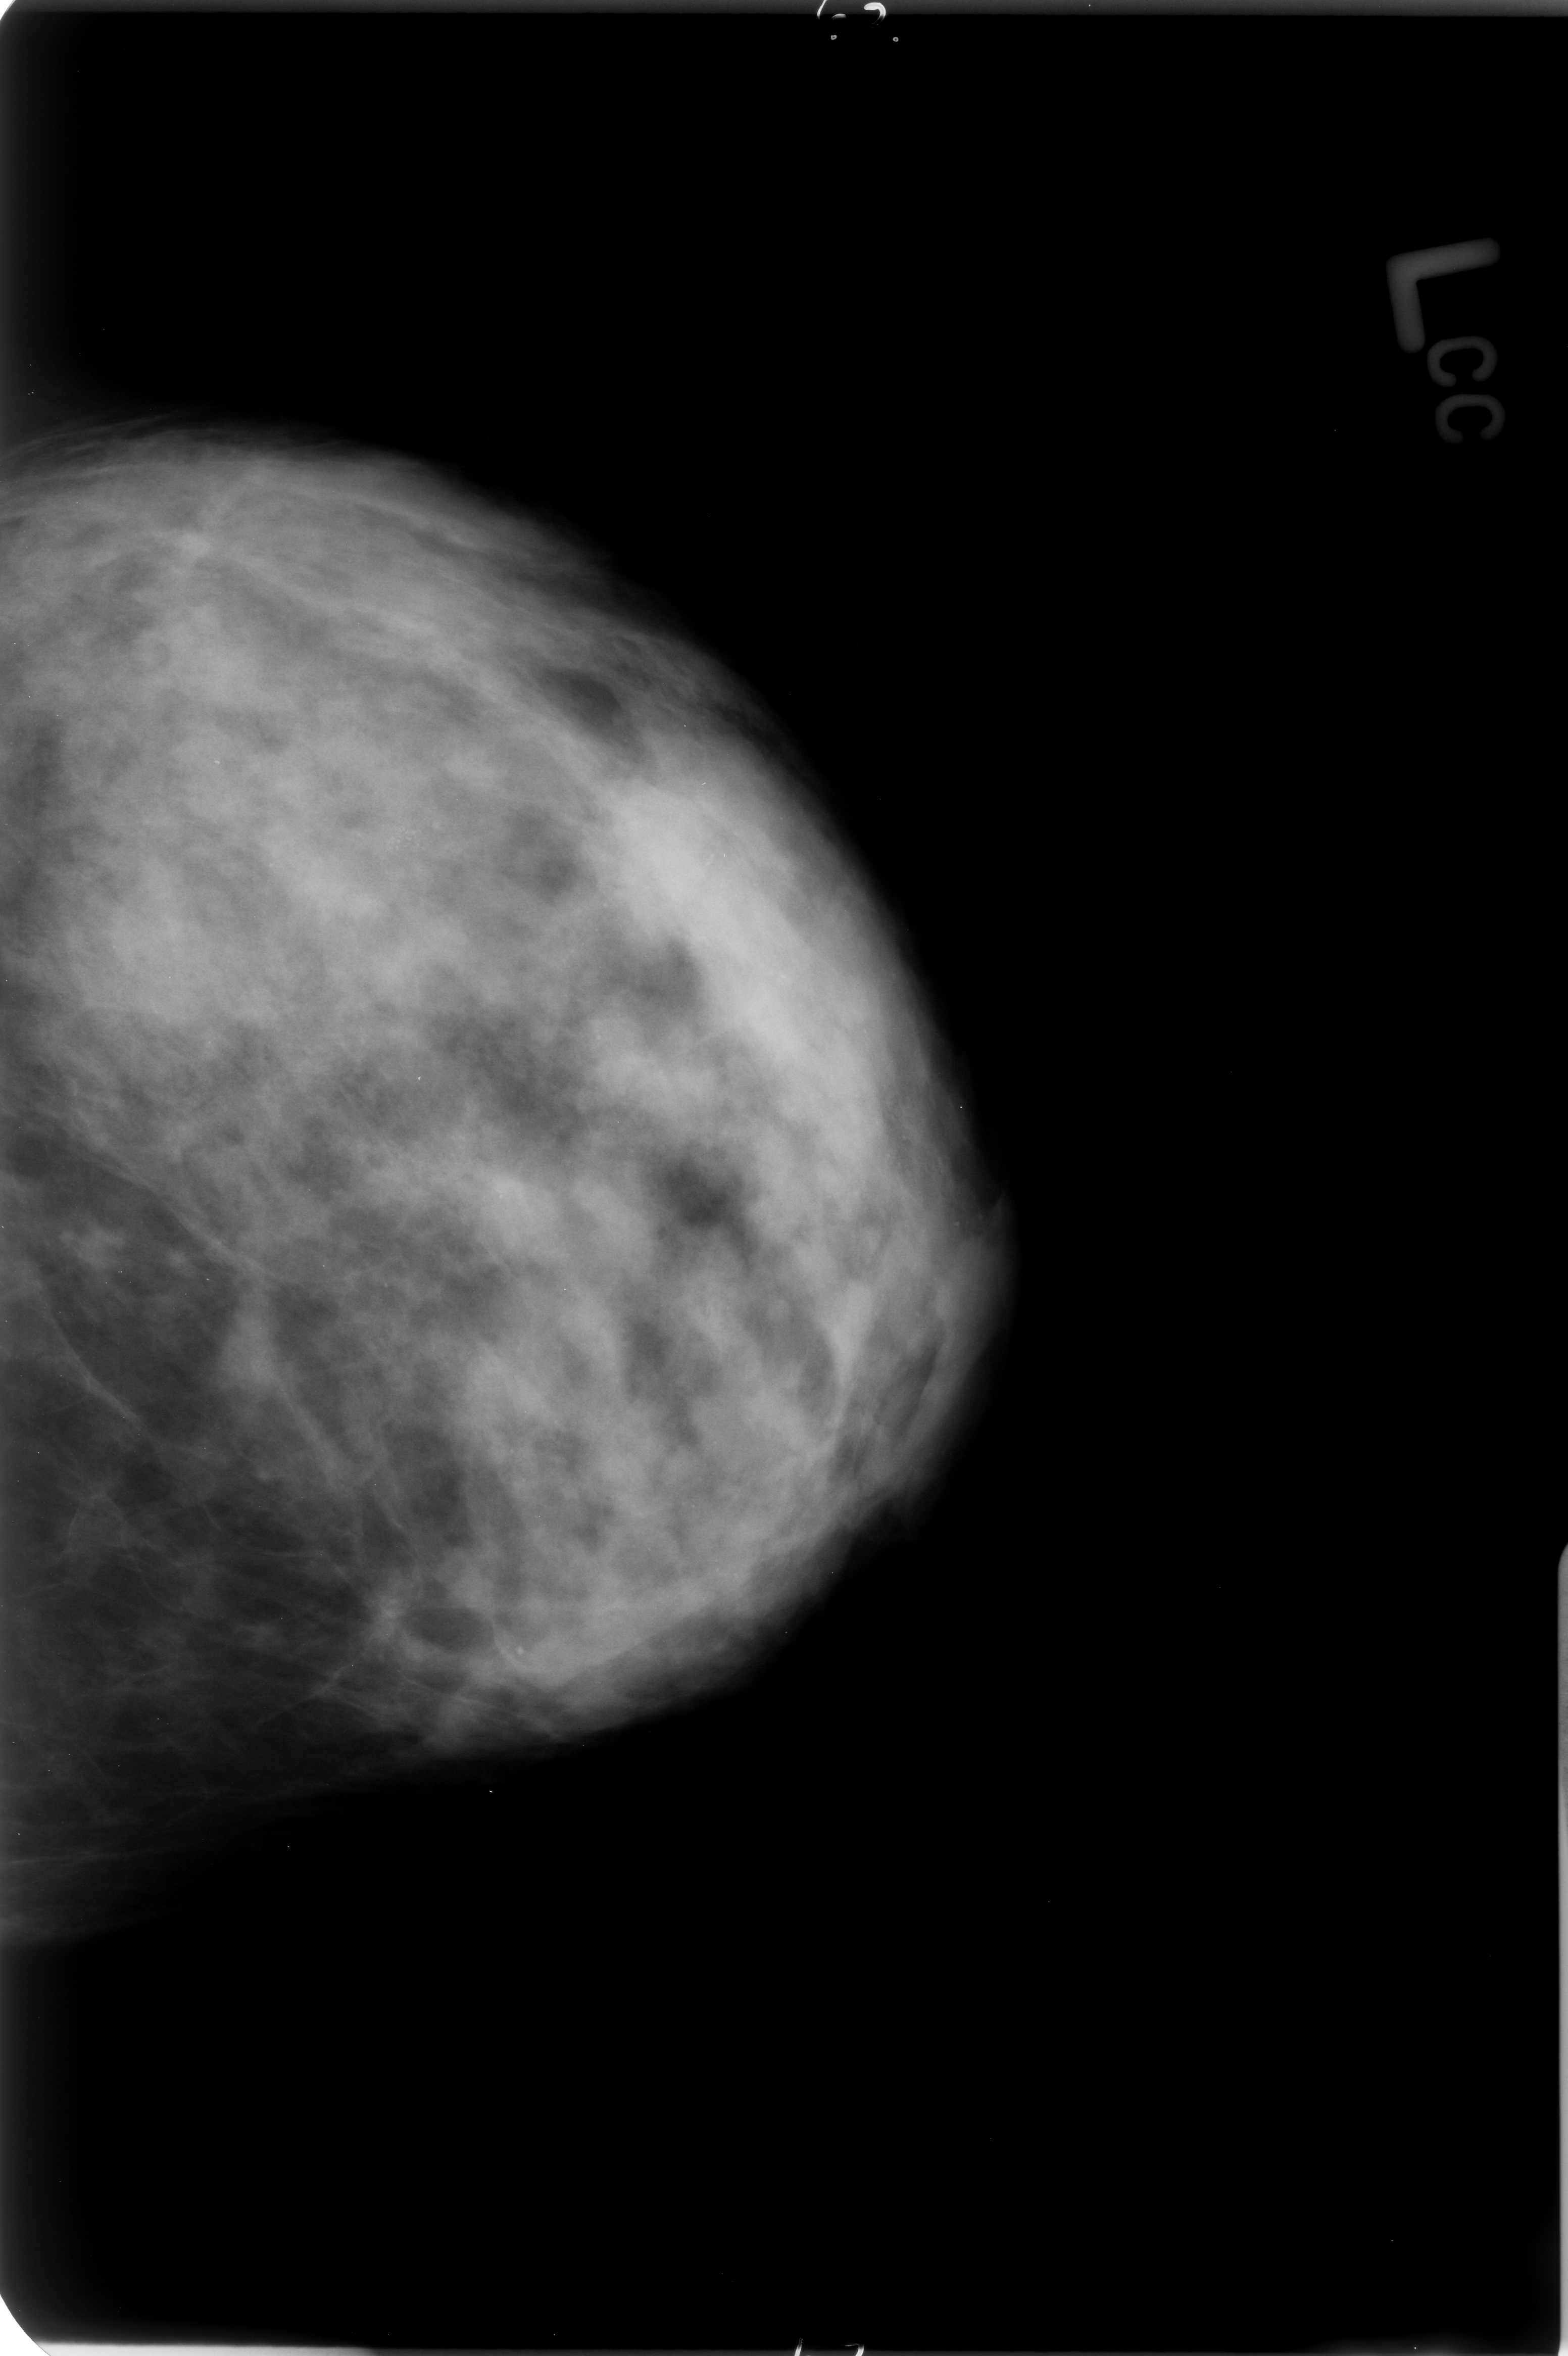
Scanned film-screen mammogram. Left breast. Craniocaudal (CC) view. Breast composition: heterogeneously dense (BI-RADS density category 3 of 4). 1568 × 2356 image matrix.
Marked abnormalities (boxes around the expert regions of interest):
- calcifications, morphology pleomorphic, distribution clustered; BI-RADS assessment category 4; pathology result (as recorded, not read from the image): benign: box from (x=355, y=775) to (x=433, y=886) px